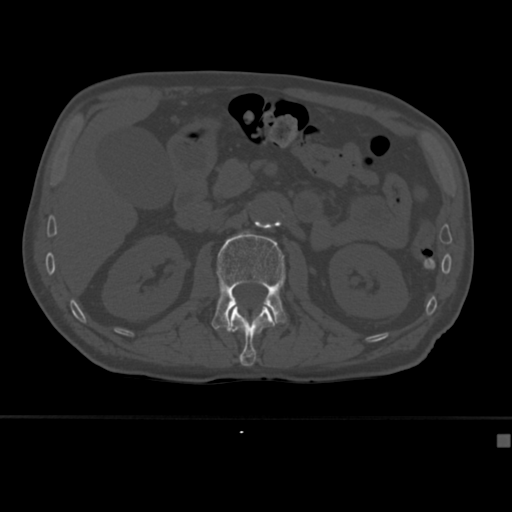
CT including the spine, one axial slice. Slice 157 of 430 in the series (ordered by position). 120 kVp. Bone window (W 1800 / L 400 HU). 1.5 mm slice thickness. 512 × 512 image matrix. Male patient, age 64 years. From the clinical record (not read from this slice): primary cancer: uterus.
Structures marked on this image (semi-automatically segmented with operator editing):
- L1 vertebra: box from (x=229, y=306) to (x=275, y=366) px
- L2 vertebra: (x=212, y=231)–(x=287, y=333)